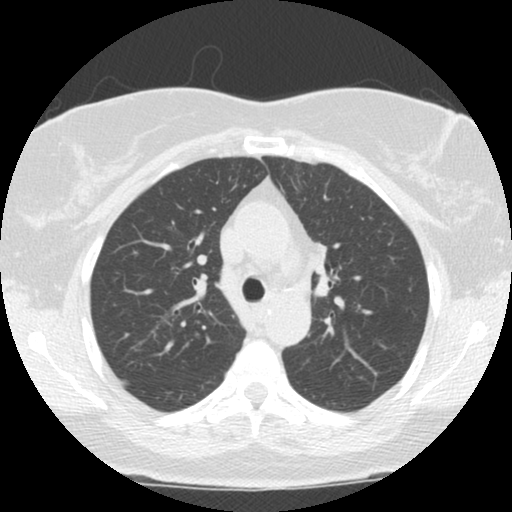
Low-dose screening chest CT, axial slice; second screening round (one year after baseline); lung window (W 1500 / L -600 HU); 2.5 mm slice thickness; 512 × 512 image matrix, field of view 310 × 310 mm. Female, age 66 years at enrolment.
- Expert reader's lesion annotation, bounding box <296,234,342,296> (left, top, right, bottom; pixels).
- Screening reader's record for this exam (one nodule recorded; not confirmed to be the boxed lesion): non-calcified nodule or mass ≥4 mm, left upper lobe, 12 × 9 mm, smooth margins, soft tissue attenuation, pre-existing on the prior screen: no.
- Official screen result: positive, other.